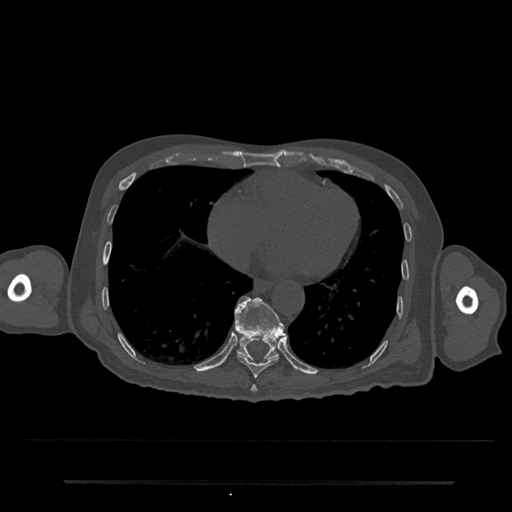
CT including the spine, one axial slice; position 344 of 797 along the scan axis; reconstruction kernel Br40s/3; 120 kVp; bone window (W 1800 / L 400 HU); 512 × 512 image matrix. Patient: male, 74 years. Case-level facts recorded for this patient, not image findings: primary cancer: prostate.
Annotated regions visible in this slice (semi-automatic segmentation, software-assisted and operator-edited):
- T10 vertebra: box from (x=235, y=296) to (x=285, y=361) px
- T8 vertebra: (x=251, y=385)–(x=258, y=392)
- T9 vertebra: (x=237, y=354)–(x=279, y=379)